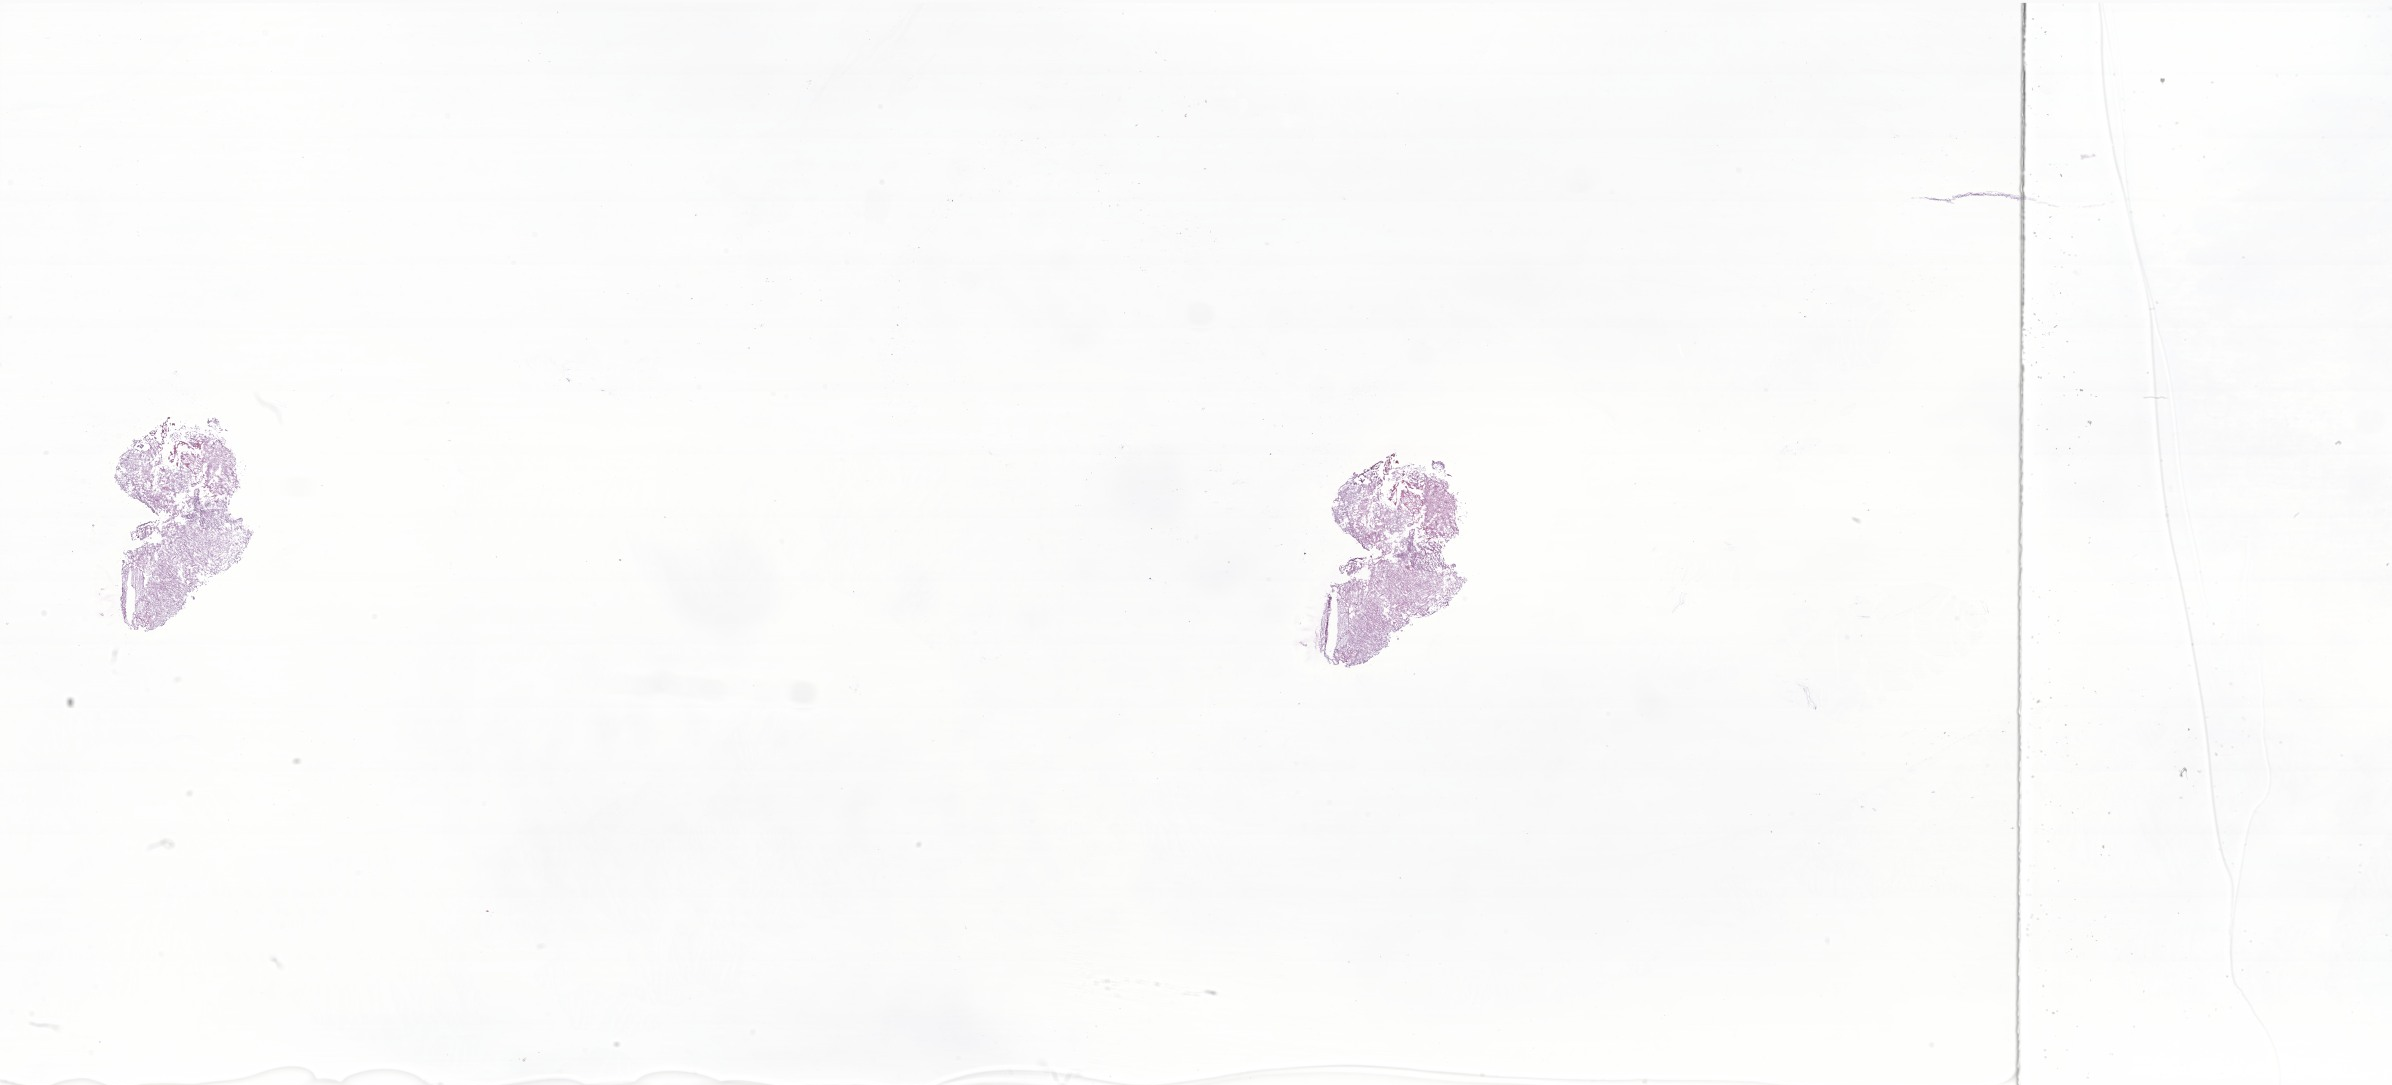
Digitized haematoxylin and eosin-stained section of tumor tissue from the brain, a low-resolution overview of the entire scanned area, about 40.3 x 18.3 mm; cryosection (OCT / tissue freezing medium). Male patient, age 211 months (17 years 7 months).
- recorded diagnosis: Ganglioglioma, NOS